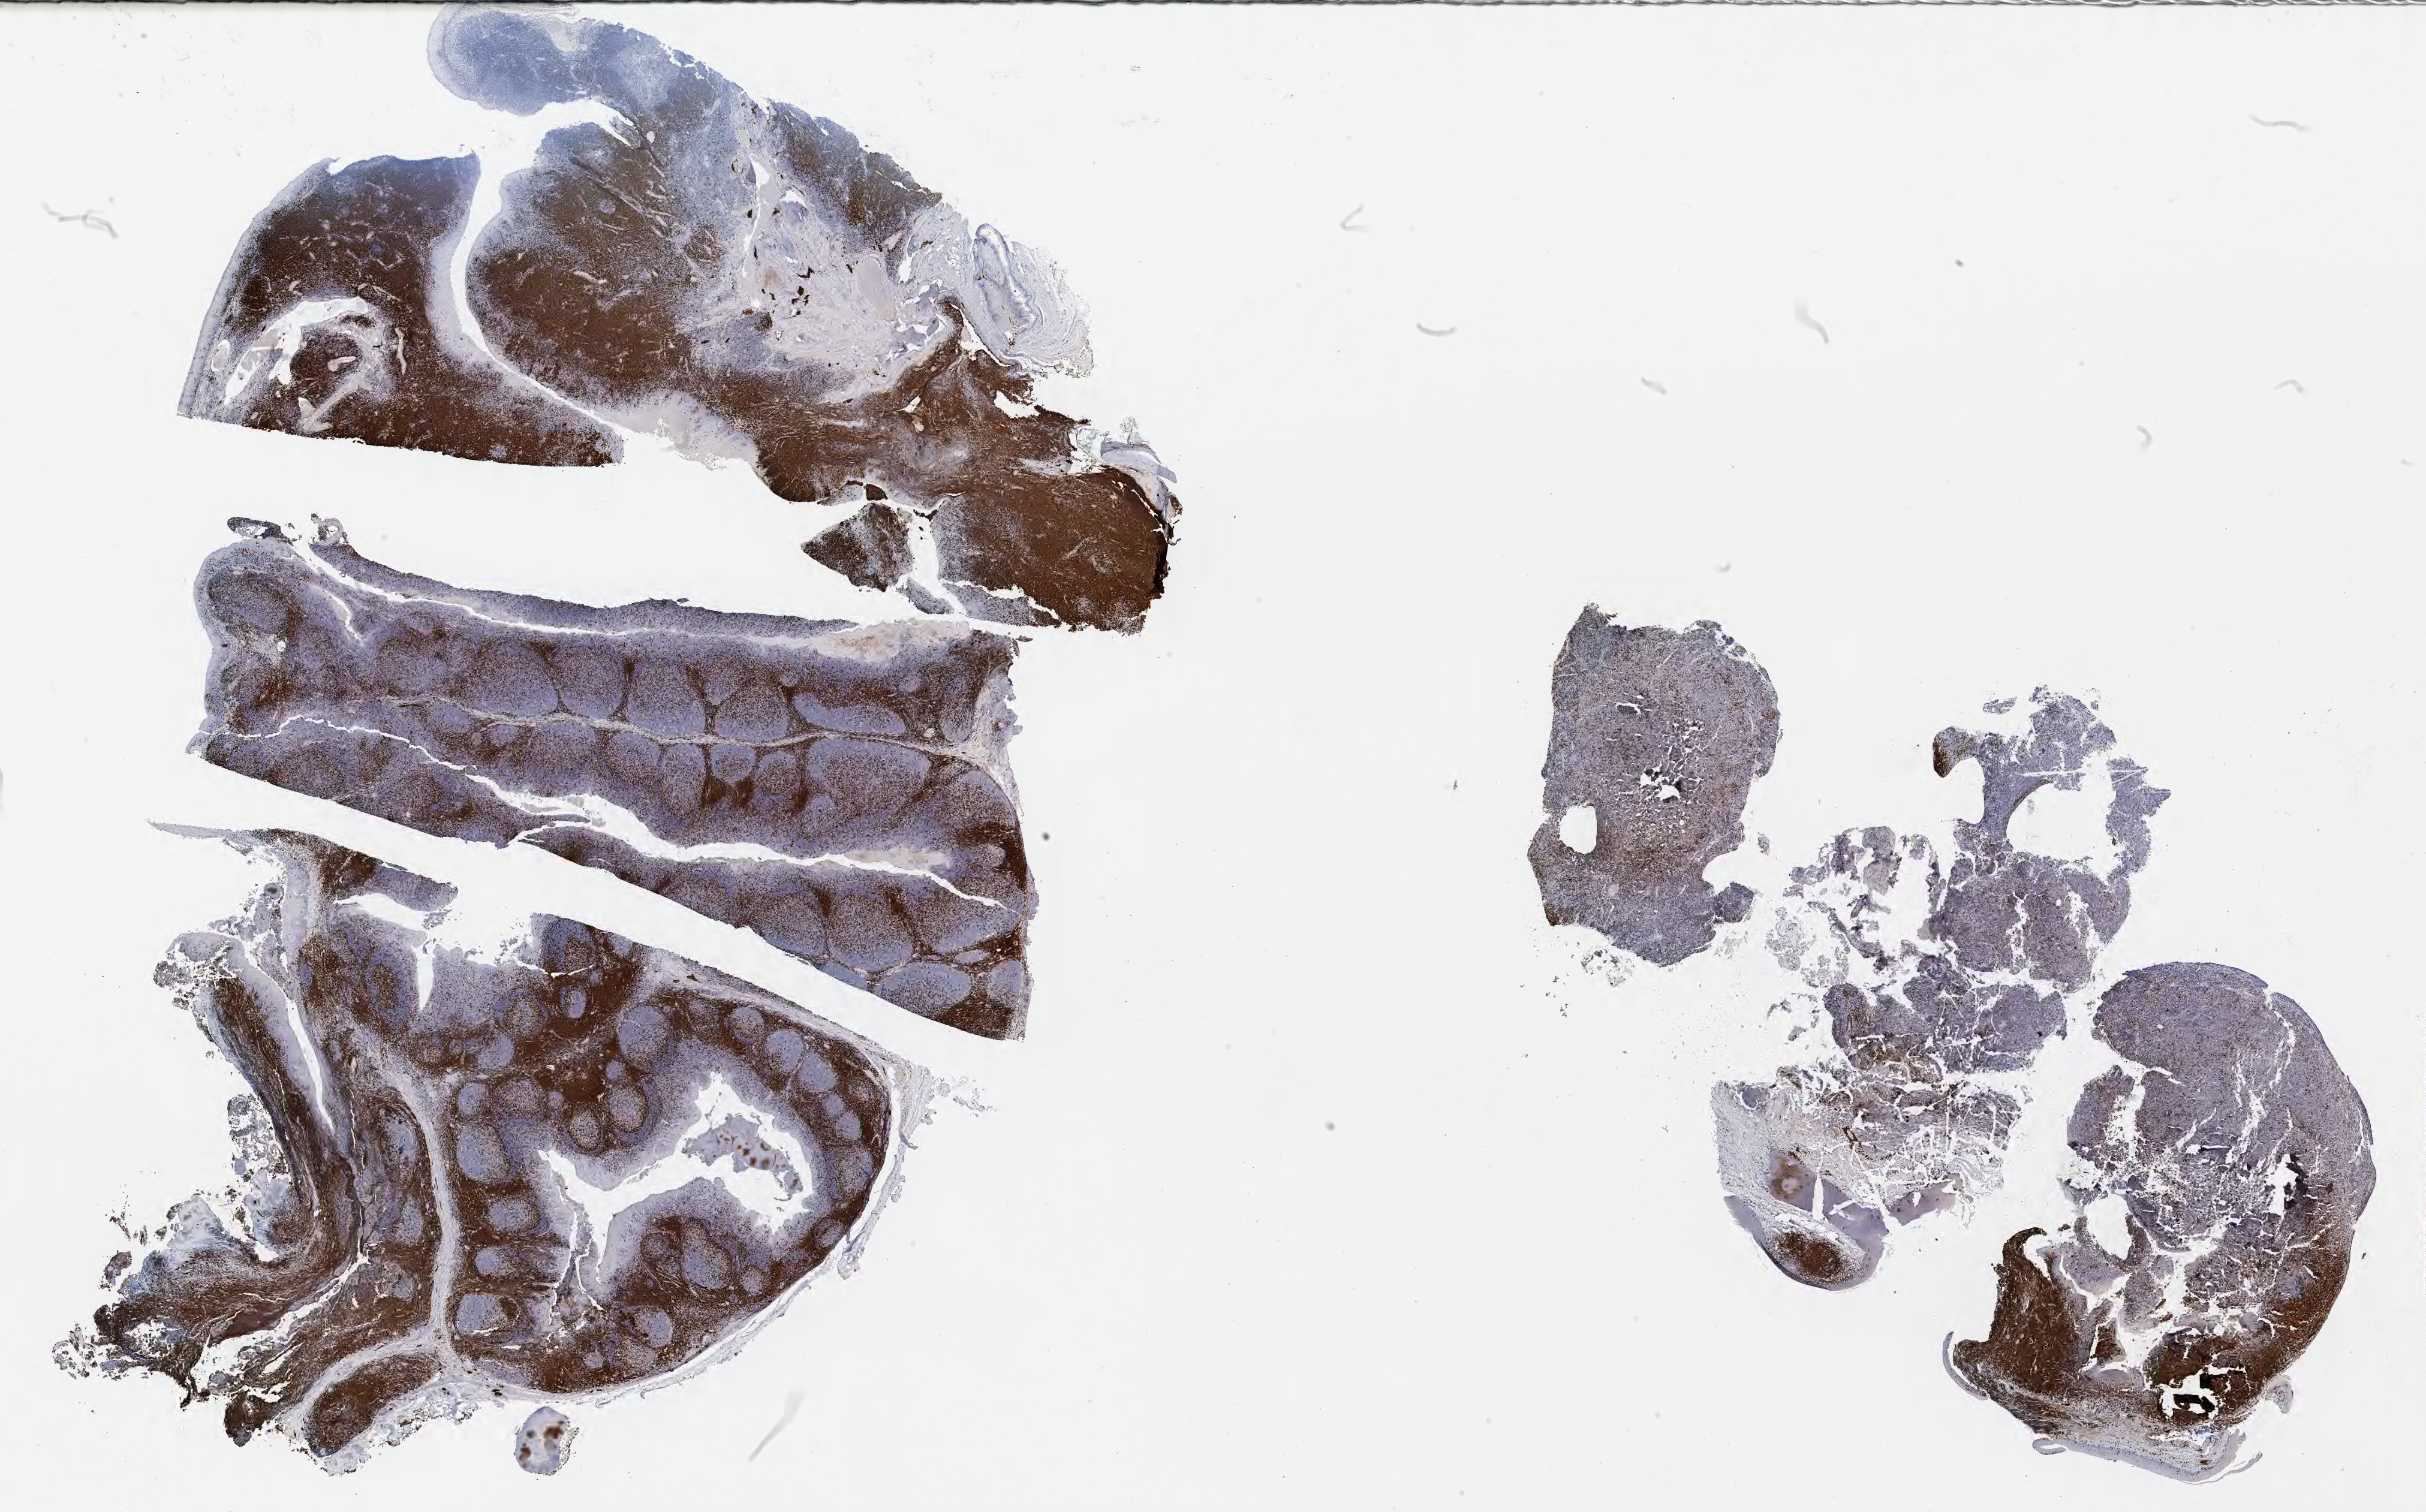
IHC for CD3, whole-slide image, low-resolution overview of the scanned area, about 32.7 x 20.4 mm. Tumor tissue. Patient: male, age 63 years.
Diagnosis: Burkitt lymphoma, NOS.